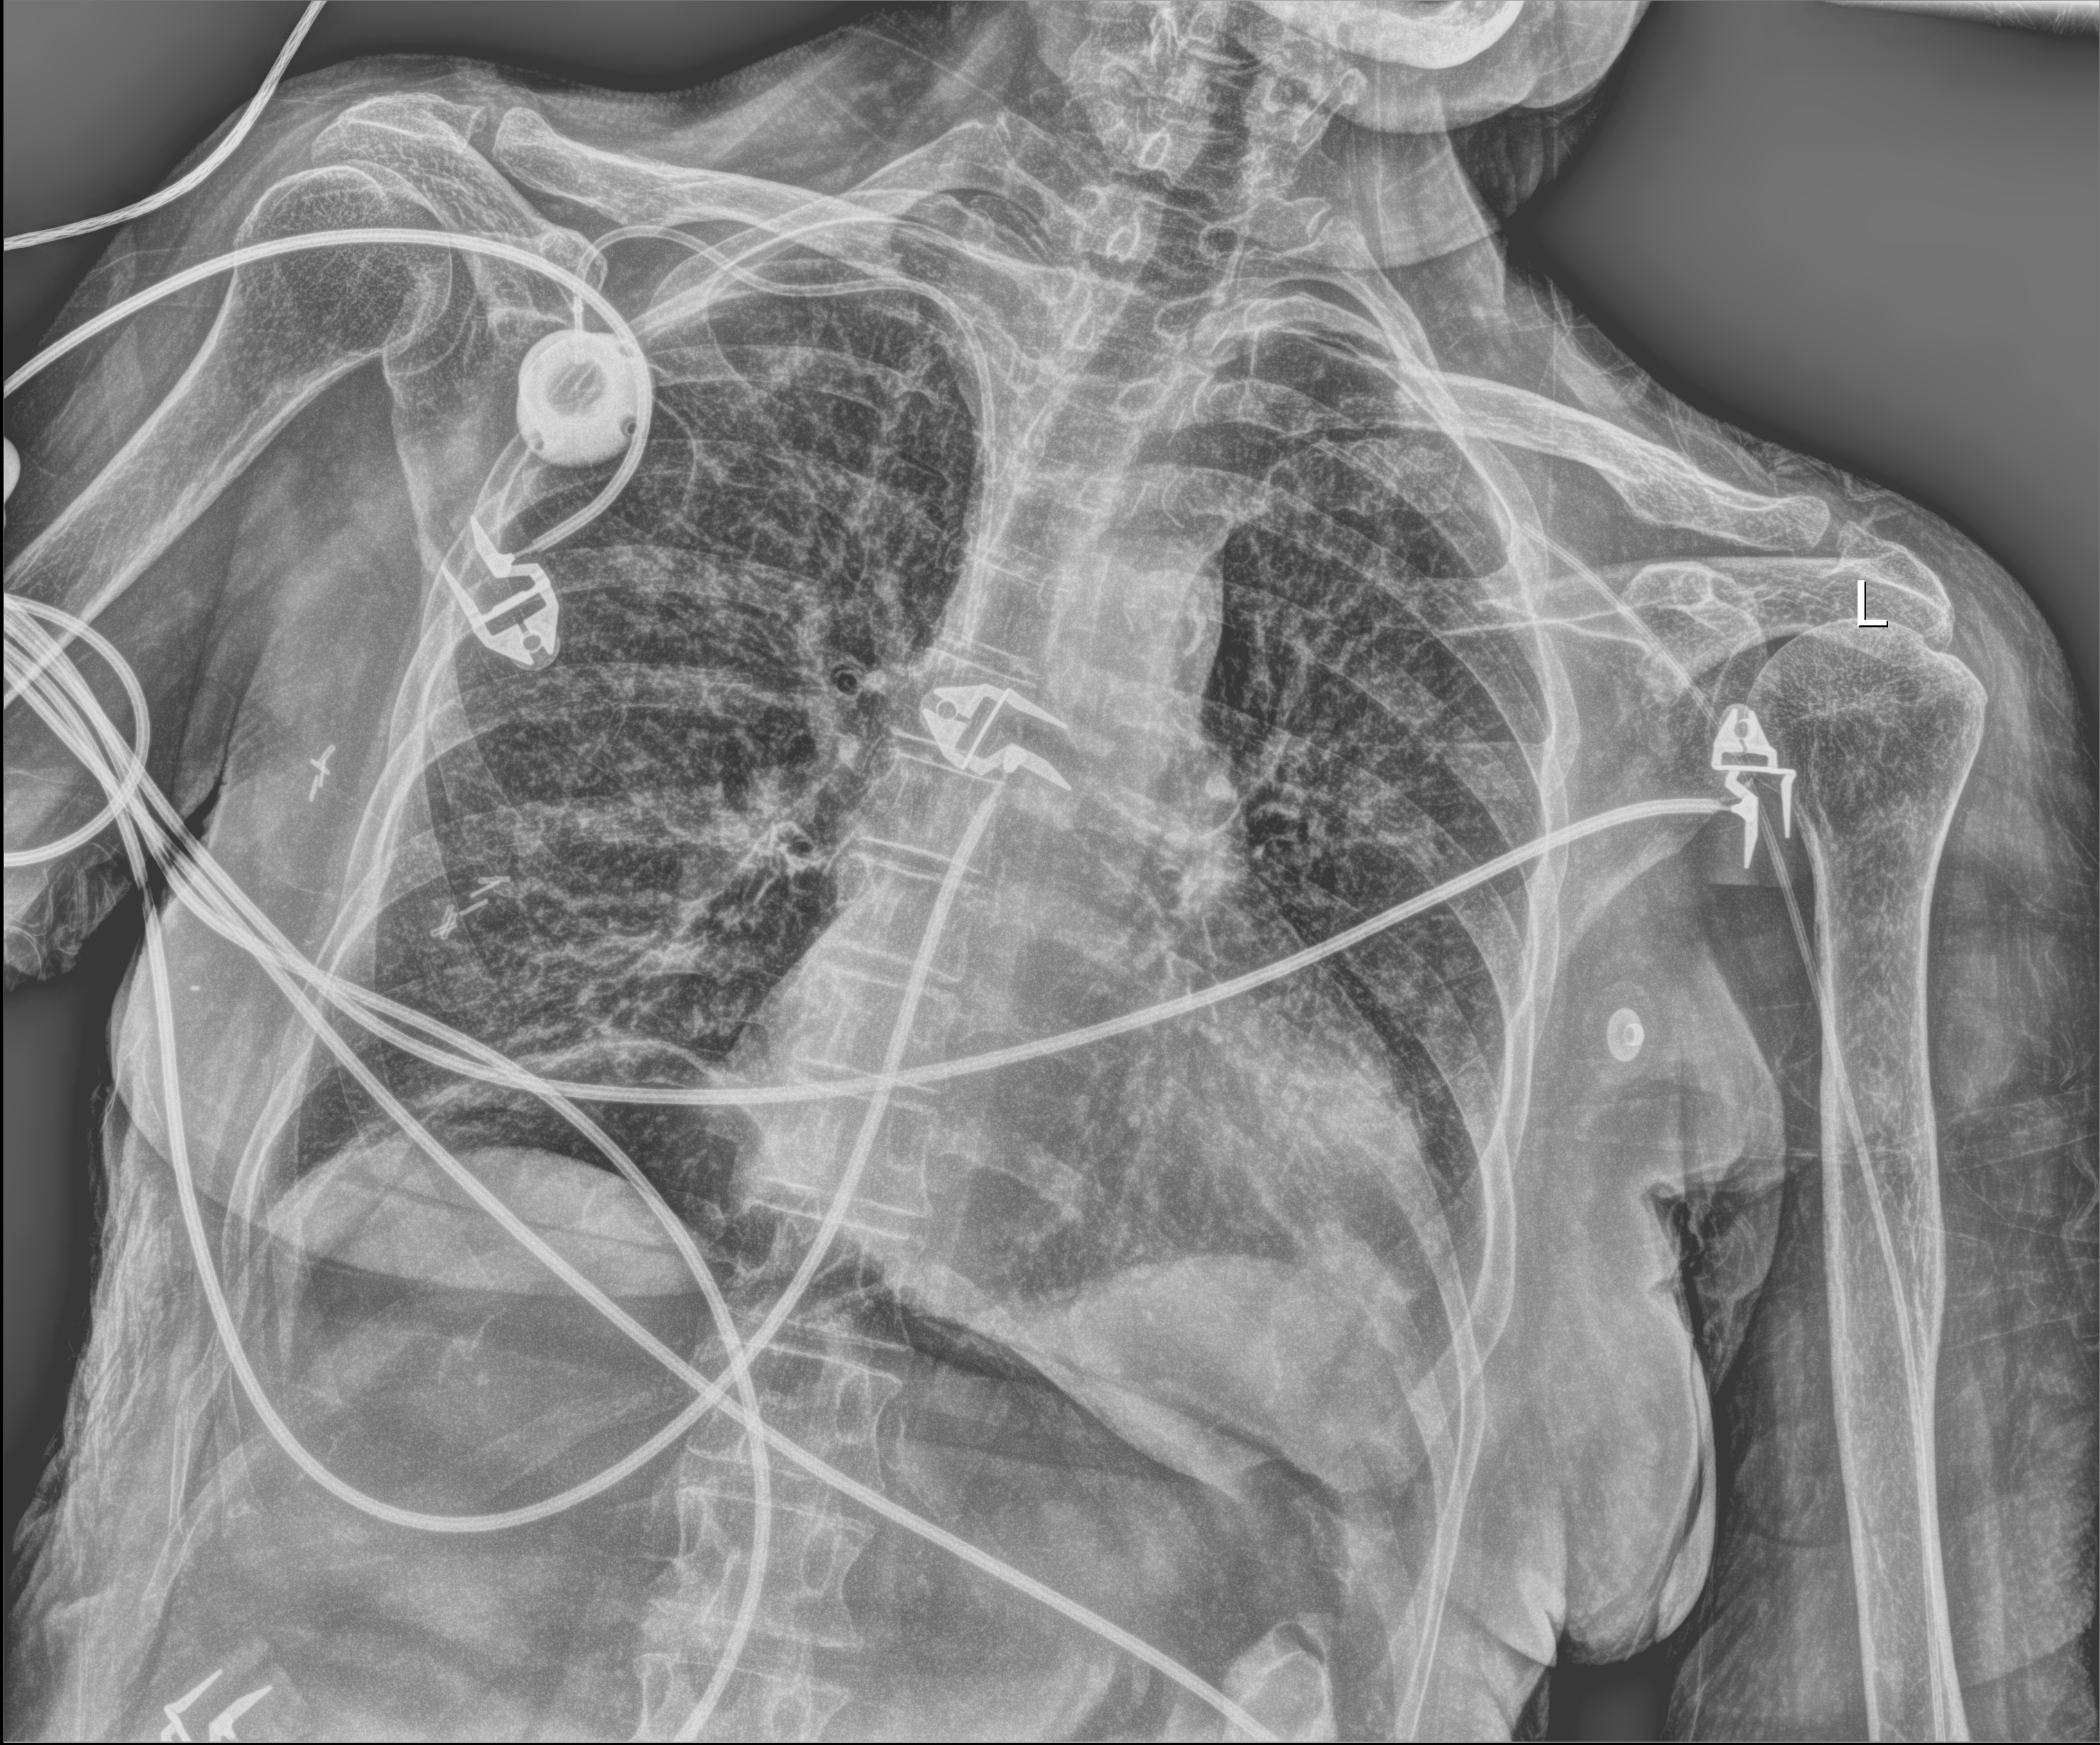
Portable chest radiograph, anteroposterior (AP) projection. Female patient hospitalised with COVID-19, age 60–74 years.
Admission-level facts for this patient (not findings on this image; timing relative to this image not recorded):
- admitted to intensive care during this hospital stay: yes